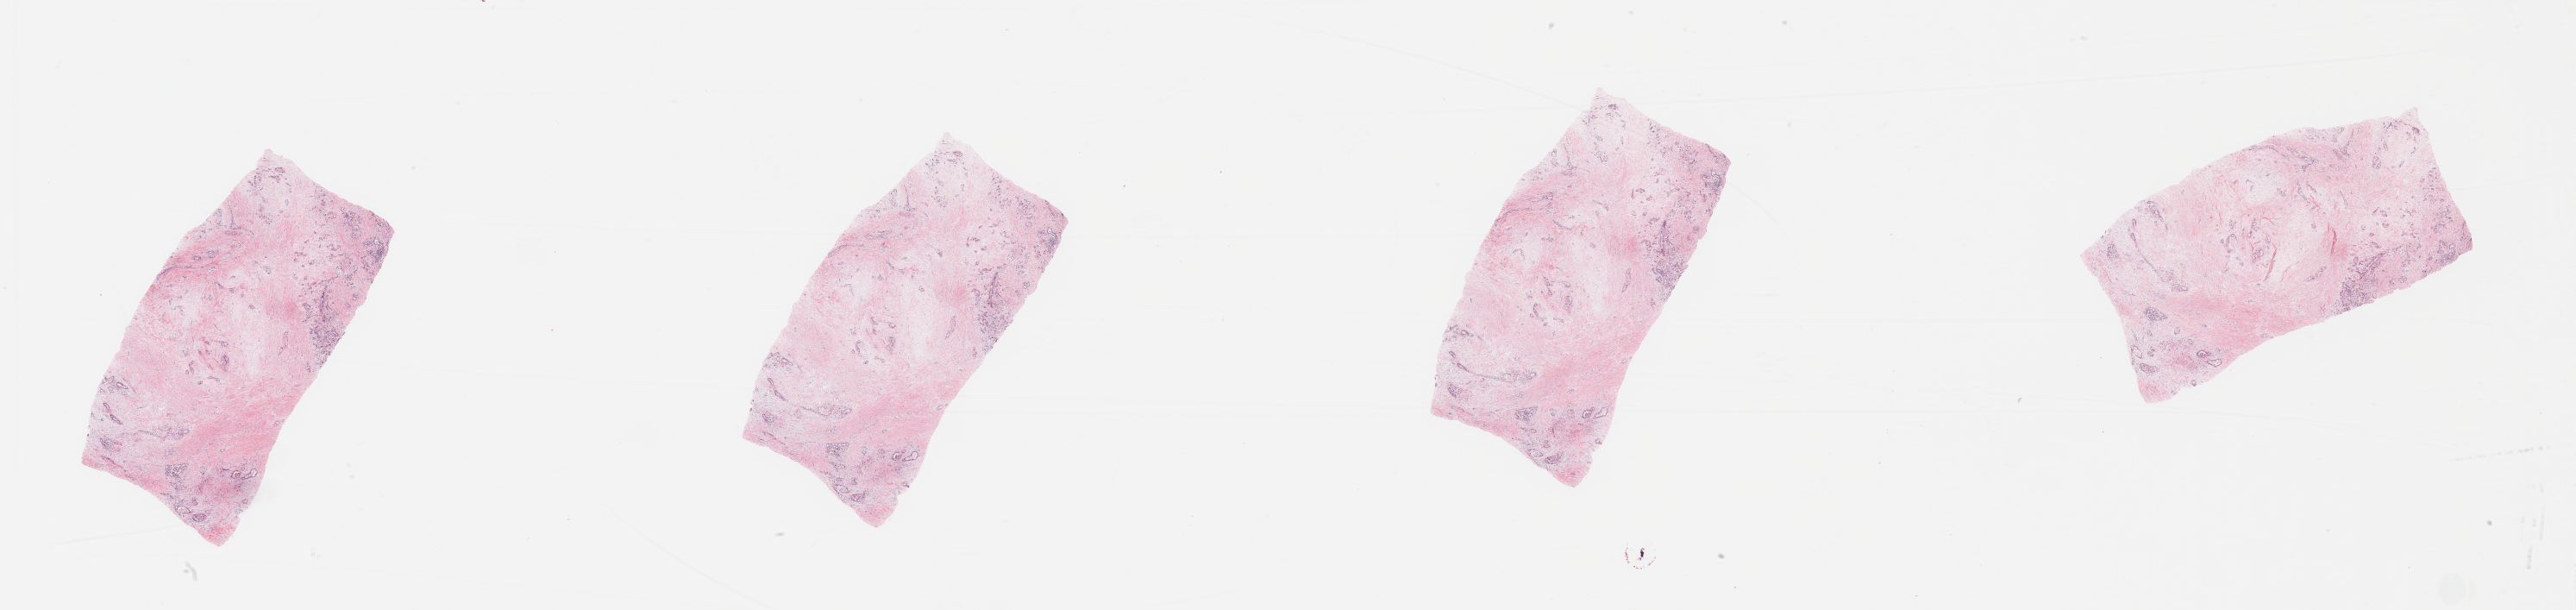
Digitized H&E-stained tissue section (whole slide) — shown as a low-resolution overview of the whole scanned area (about 47.3 x 11.2 mm, from a 20x scan). Tumour tissue sample, sampled site: pancreas. 63-year-old male patient. Histologic grade: G2 (moderately differentiated). Composition of this section per pathologist review: tumour nuclei 20%, necrosis 0%.
Histologic diagnosis: Infiltrating duct carcinoma, NOS. AJCC pathologic stage: IB. Primary tumour site (as recorded): tail.